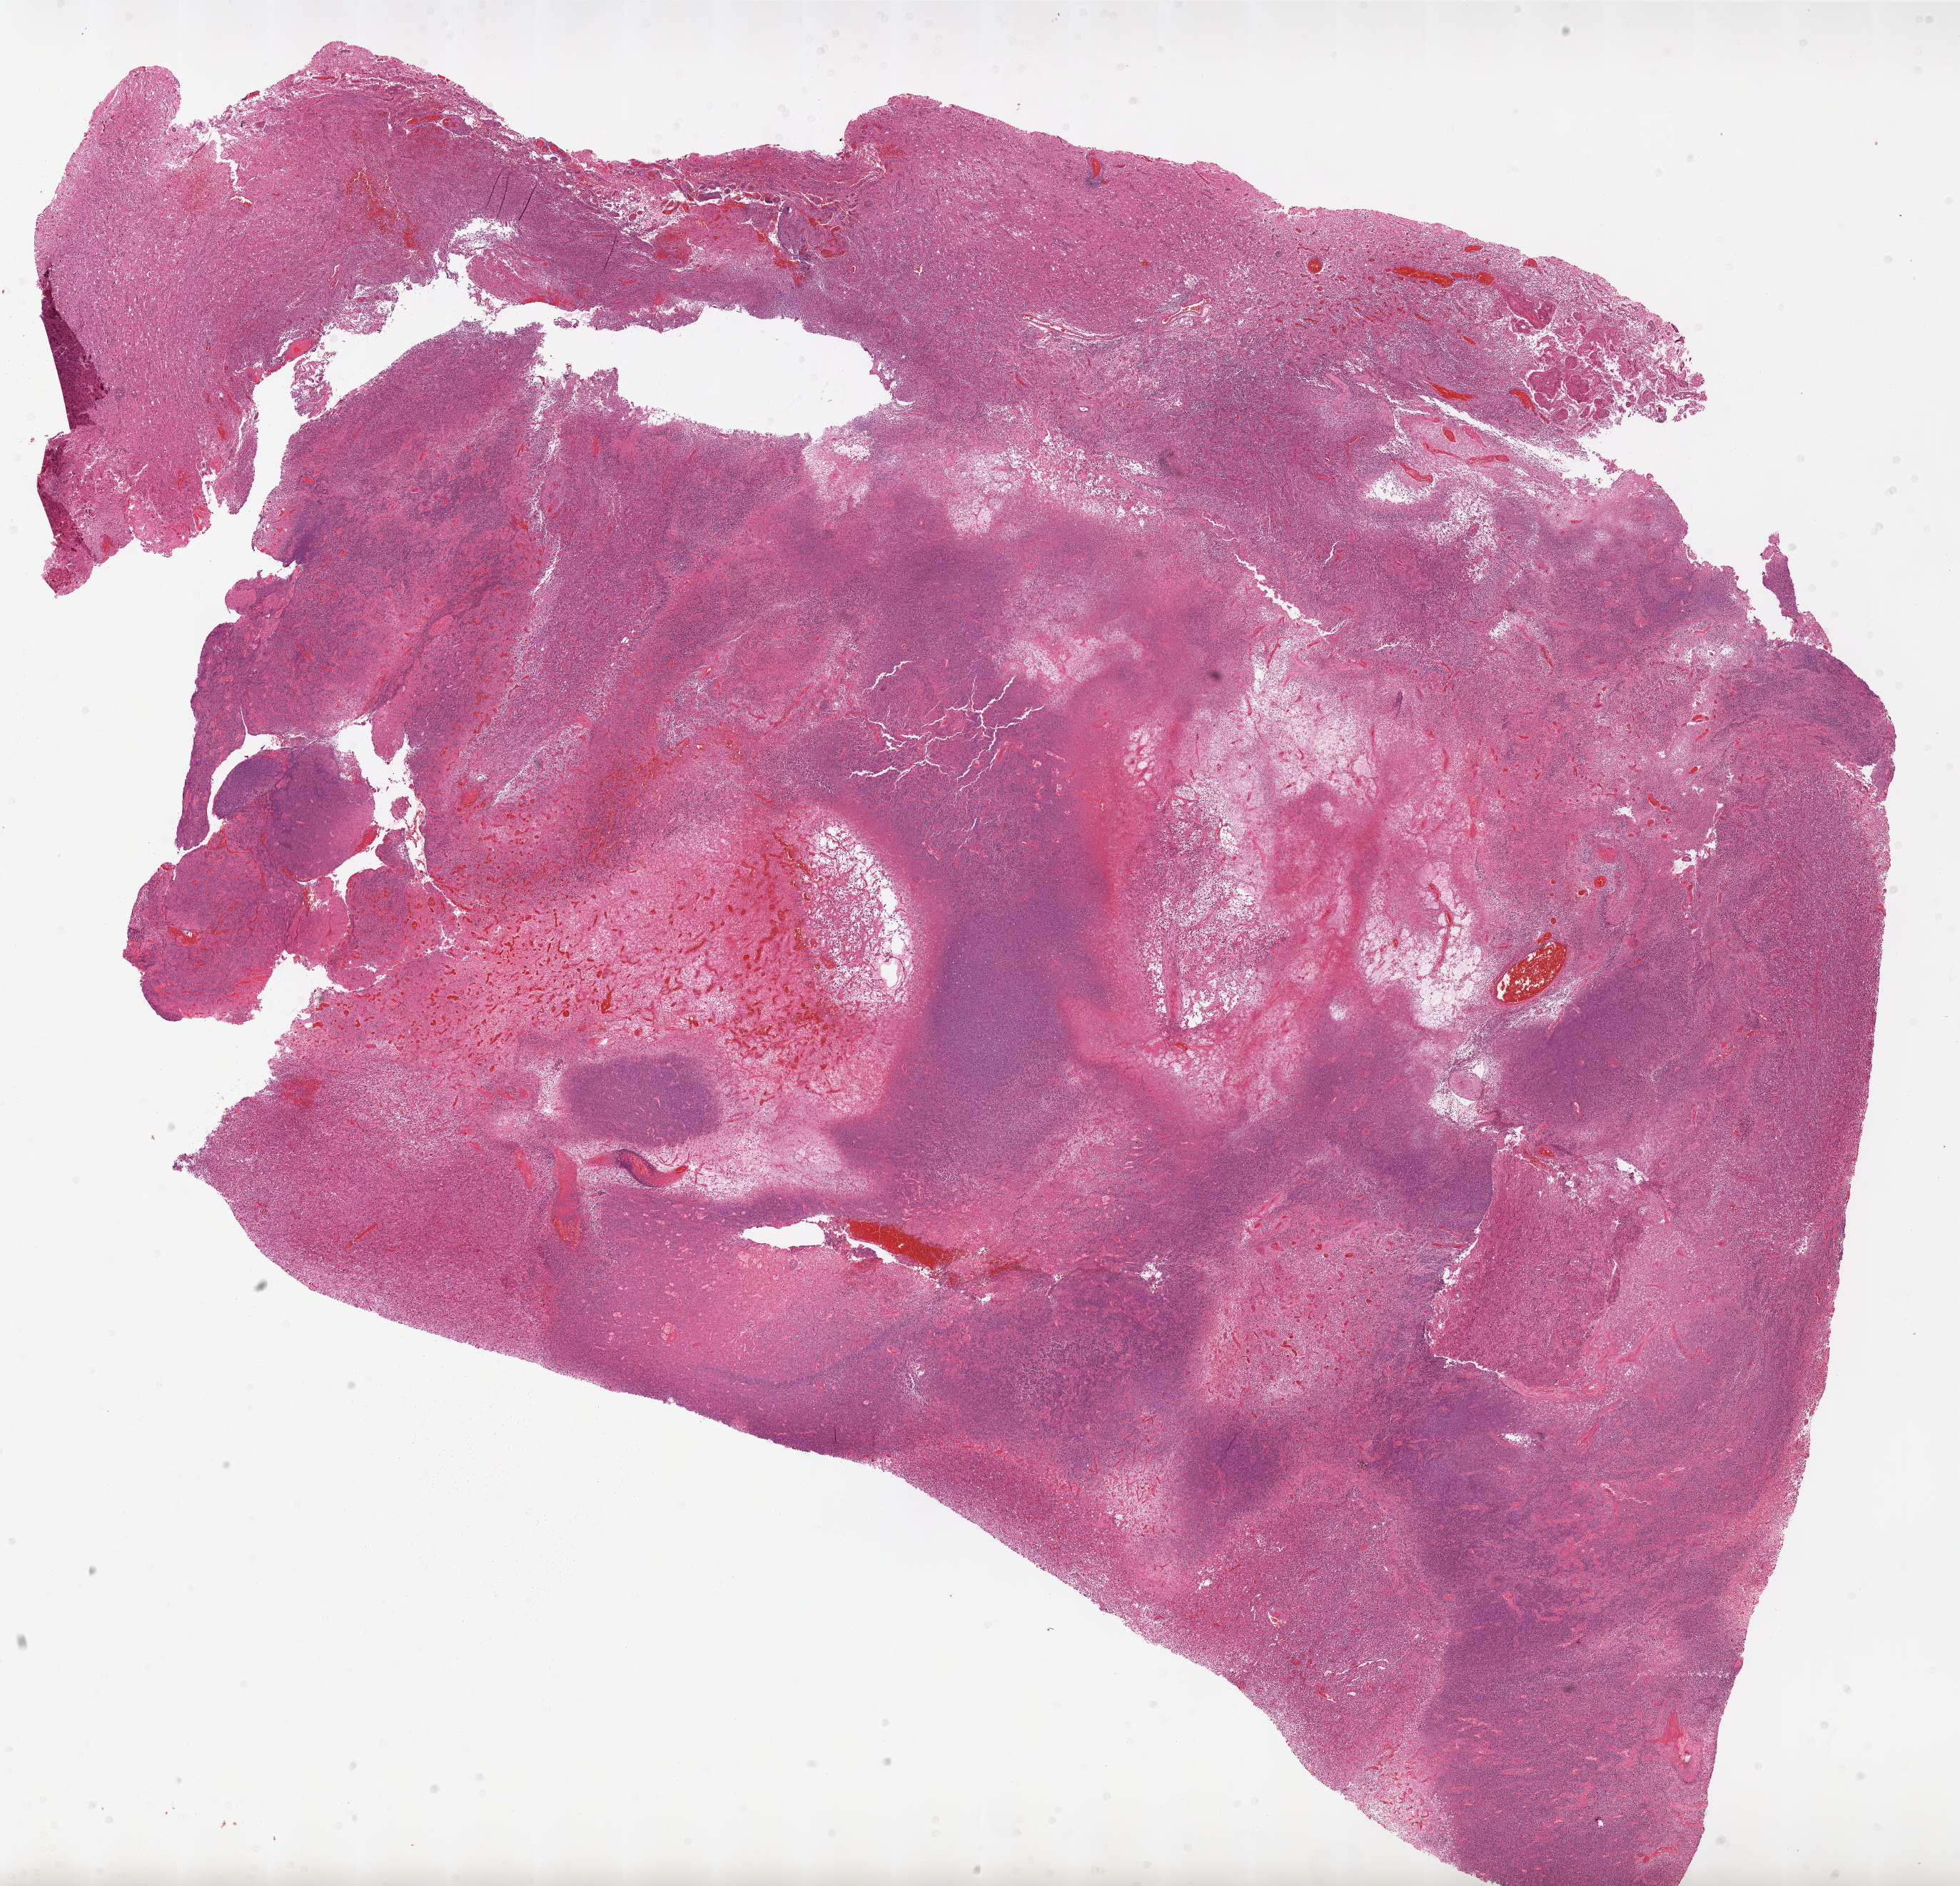
Whole-slide histology image, H&E-stained — low-resolution overview of the scanned area, about 22.0 x 21.2 mm (acquisition: 20x scan); formalin-fixed paraffin-embedded (FFPE) diagnostic section; primary tumour sample from the brain. Female, age 52 years at initial diagnosis.
Histologic diagnosis: Glioblastoma.